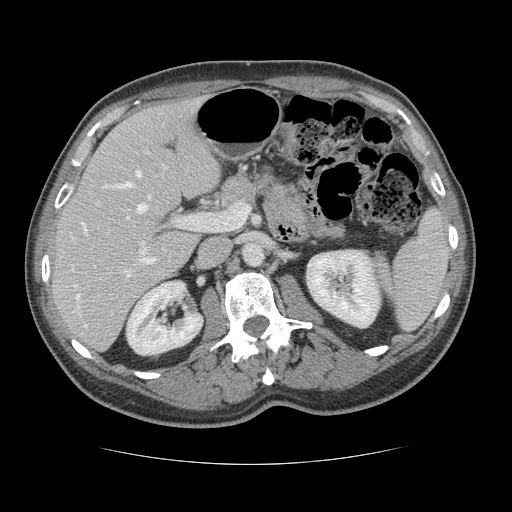
Contrast-enhanced abdominal CT, one axial slice. Position 72 of 134 along the scan axis. Reconstruction kernel STANDARD. Intravenous contrast given. Soft-tissue window (W 400 / L 40 HU). 2.5 mm slice thickness. 512 × 512 image matrix. Male patient, age 68 years. Case-level facts recorded for this patient, not image findings: diagnosis: colorectal cancer liver metastases, imaged before liver resection; multiple liver metastases: yes.
Outlined on this slice (outlined manually by an expert reader):
- hepatic veins: bounding box <74,170,151,327> (left, top, right, bottom; pixels)
- liver: <53,100,219,350>
- planned liver remnant (the part of the liver to remain after resection): <53,100,219,337>
- portal vein (with intrahepatic branches): <124,216,197,277>